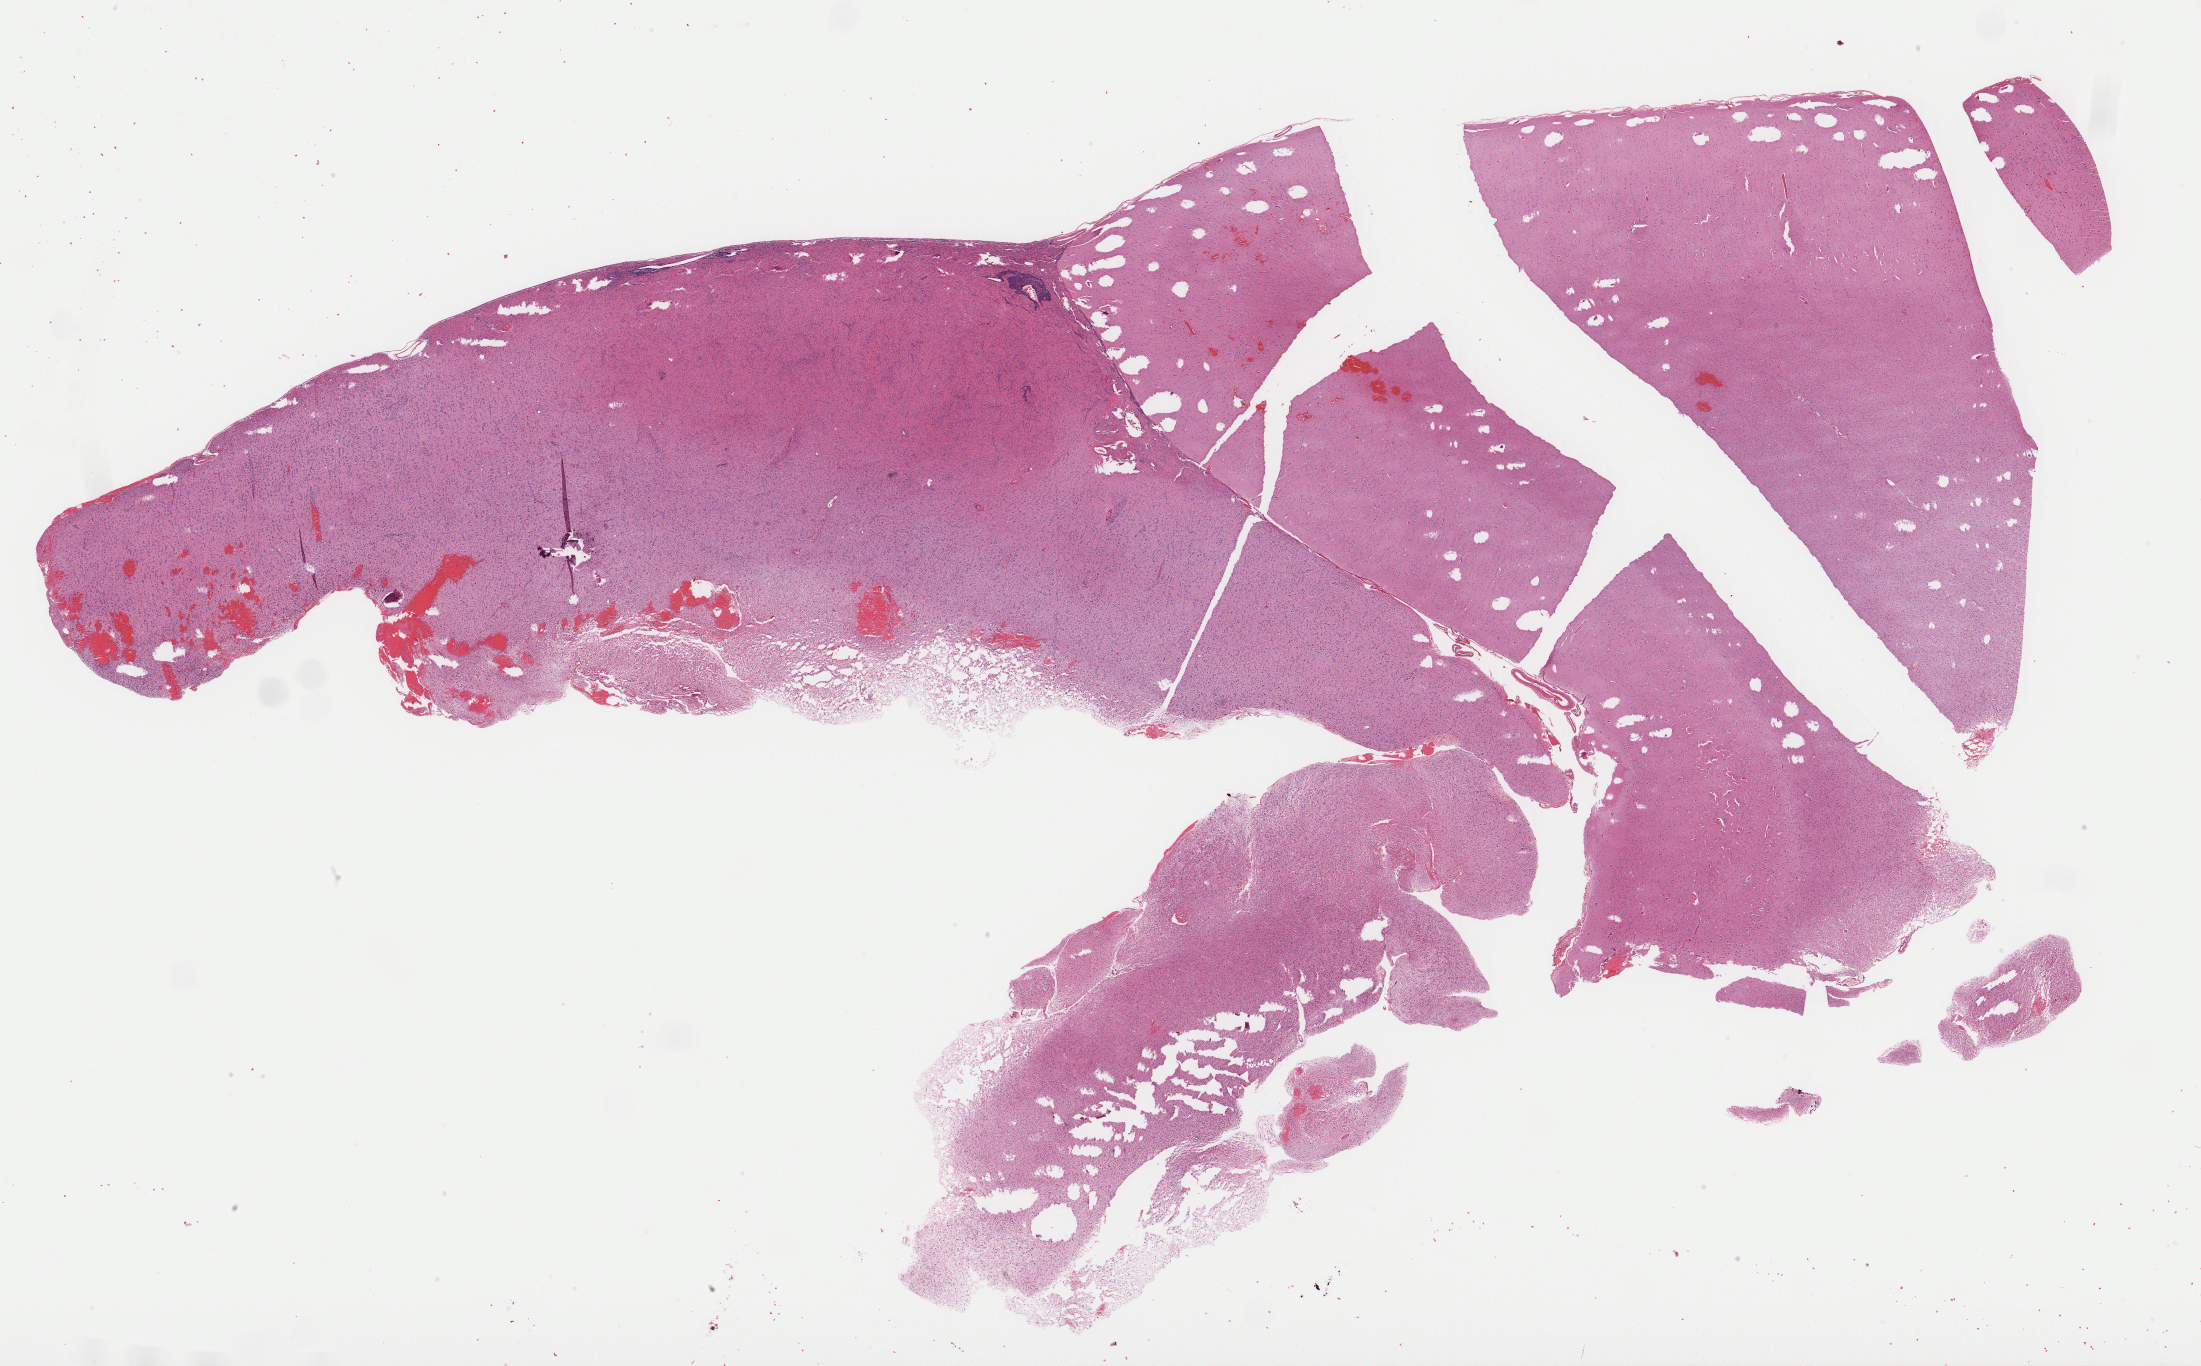
Digitized H&E-stained tissue section (whole slide) — a low-resolution overview of the entire scanned area, about 34.7 x 21.5 mm (from a 40x scan); formalin-fixed paraffin-embedded (FFPE) diagnostic section; sample: primary tumour, brain. Patient: male, age at initial diagnosis 38 years. Histologic grade: G3 (poorly differentiated).
Diagnosis: Astrocytoma, anaplastic.